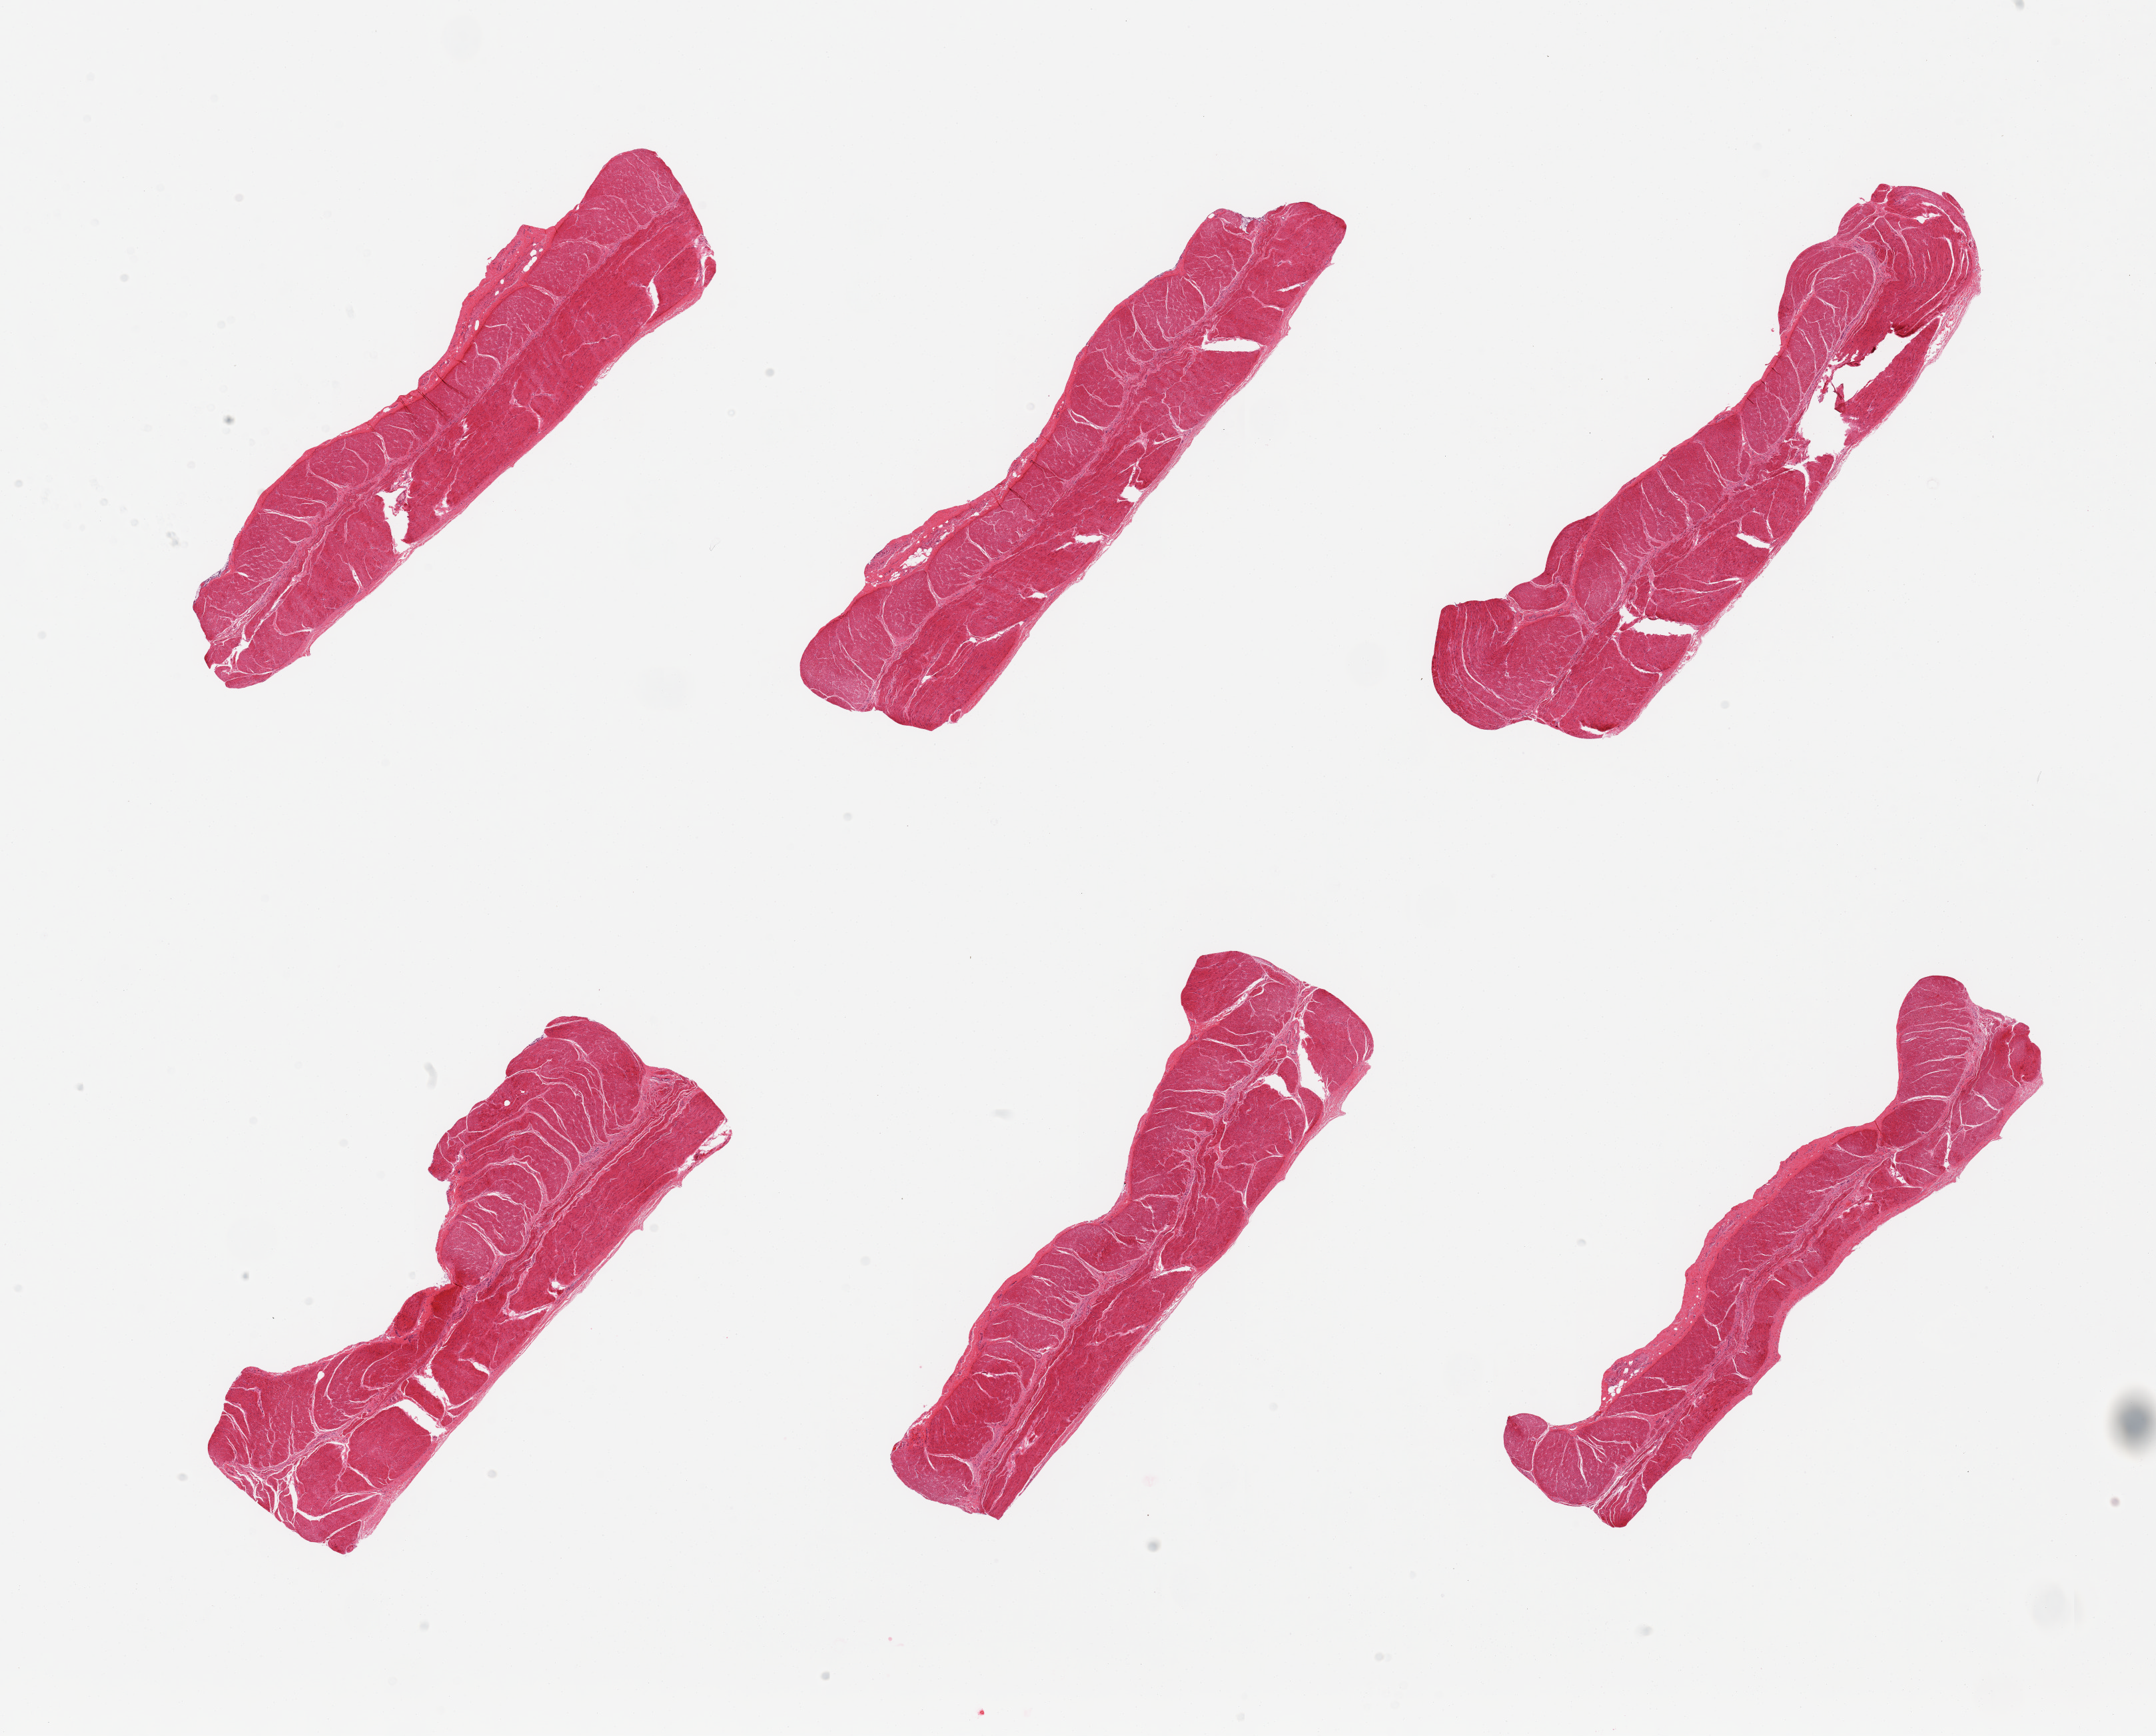
Digitized H&E-stained section — a low-resolution overview of the entire scanned area, about 25.6 x 20.6 mm. PAXgene-fixed paraffin-embedded (PFPE) section. Sampled site (target tissue): sigmoid colon. Donor tissue sample.
Reviewer comment on this tissue sample: 6 pieces; well trimmed.